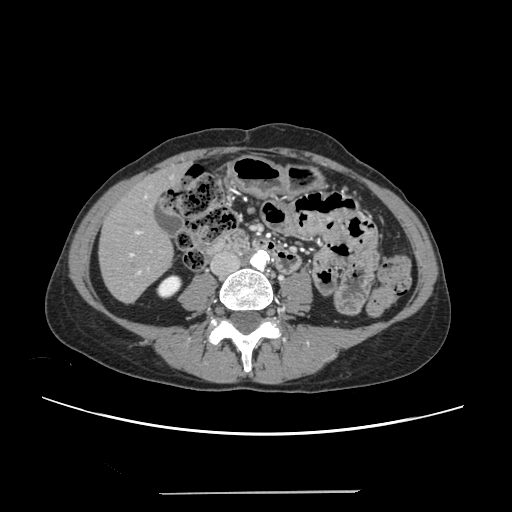
Contrast-enhanced abdominal CT, one axial slice. Slice 61 of 240 in the series (ordered by position). 120 kVp. Soft-tissue window (W 400 / L 40 HU). 1.25 mm slice thickness. 512 × 512 image matrix. Female patient, age 60 years. Case-level facts recorded for this patient, not image findings: diagnosis: colorectal cancer liver metastases, imaged before liver resection; multiple liver metastases: no; largest metastasis: 1.5 cm; disease in both lobes: no.
Annotated regions visible in this slice (expert manual segmentation):
- liver: bounding box (x1, y1, x2, y2) in pixels: (100, 168, 183, 302)
- planned liver remnant (the part of the liver to remain after resection): (100, 172, 173, 302)
- portal vein (with intrahepatic branches): (129, 193, 149, 274)